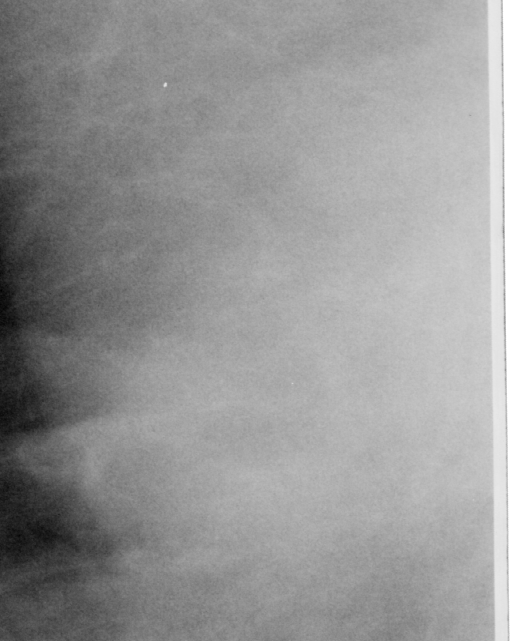
Region of interest cut from a scanned film mammogram (one marked finding); right breast; MLO view; BI-RADS breast density category 3 (scale 1–4).
- Mass, shape focal asymmetric density; BI-RADS assessment category 2; benign; no additional work-up was recommended (benign without callback).